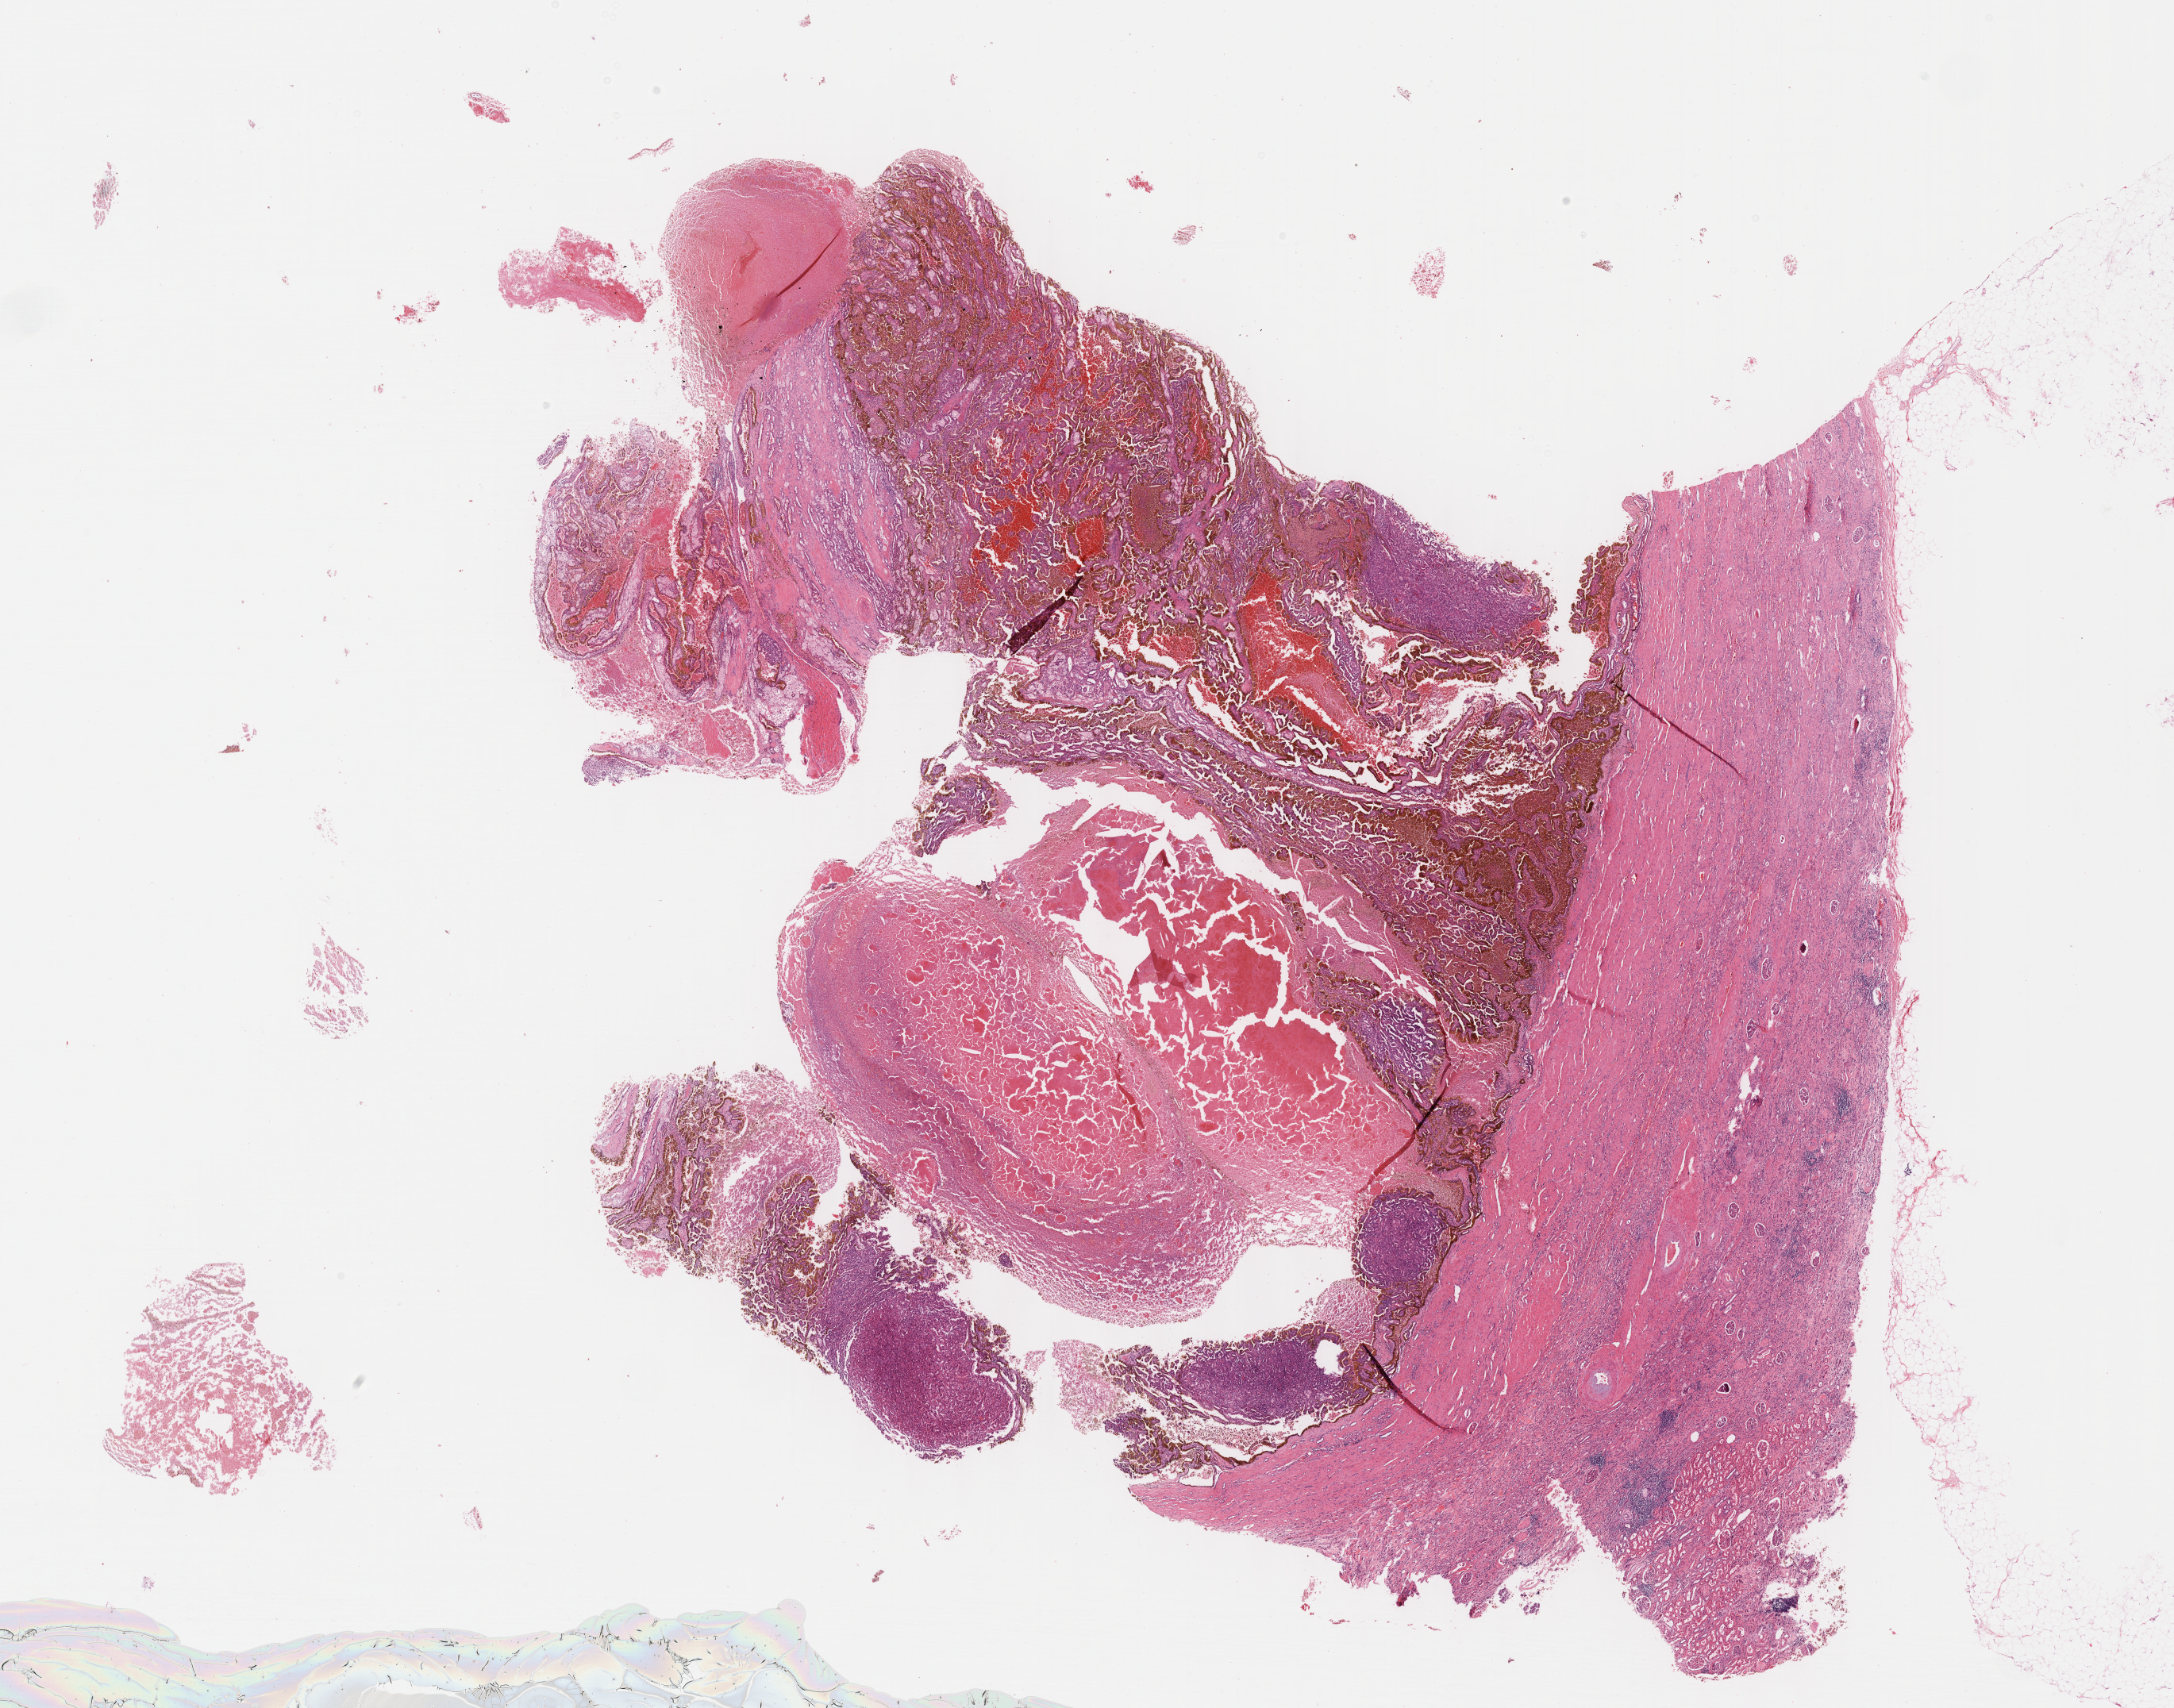
Digitized H&E tissue section (whole slide), low-resolution overview of the scanned area, about 22.1 x 17.4 mm (acquisition: 40x scan). Formalin-fixed paraffin-embedded (FFPE) diagnostic section. Sample: primary tumour, kidney. Male, age 62 years at initial diagnosis.
Laterality: left. AJCC pathologic stage: II. TNM: T2 N0 MX. Histologic diagnosis: Papillary adenocarcinoma, NOS.